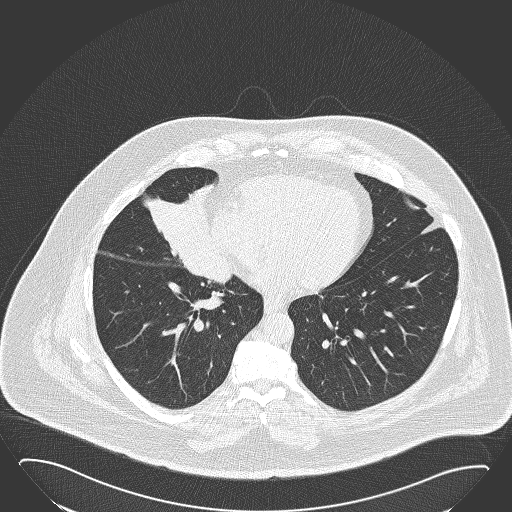
Chest CT (low-dose screening protocol), one axial image, baseline screening round, lung window (W 1500 / L -600 HU), slice 101 of 168 in the series. Male participant, aged 61 years at enrolment. Former smoker at enrolment.
Lesion marked by an expert reader, bounding box <136,178,228,267> (left, top, right, bottom; pixels). The screening reader recorded 2 non-calcified nodules or masses ≥4 mm on this exam; which of them this box marks is not recorded. Official screen result: positive, change unspecified: nodule(s) >= 4 mm or enlarging nodule(s), mass(es), or other non-specific abnormalities suspicious for lung cancer.